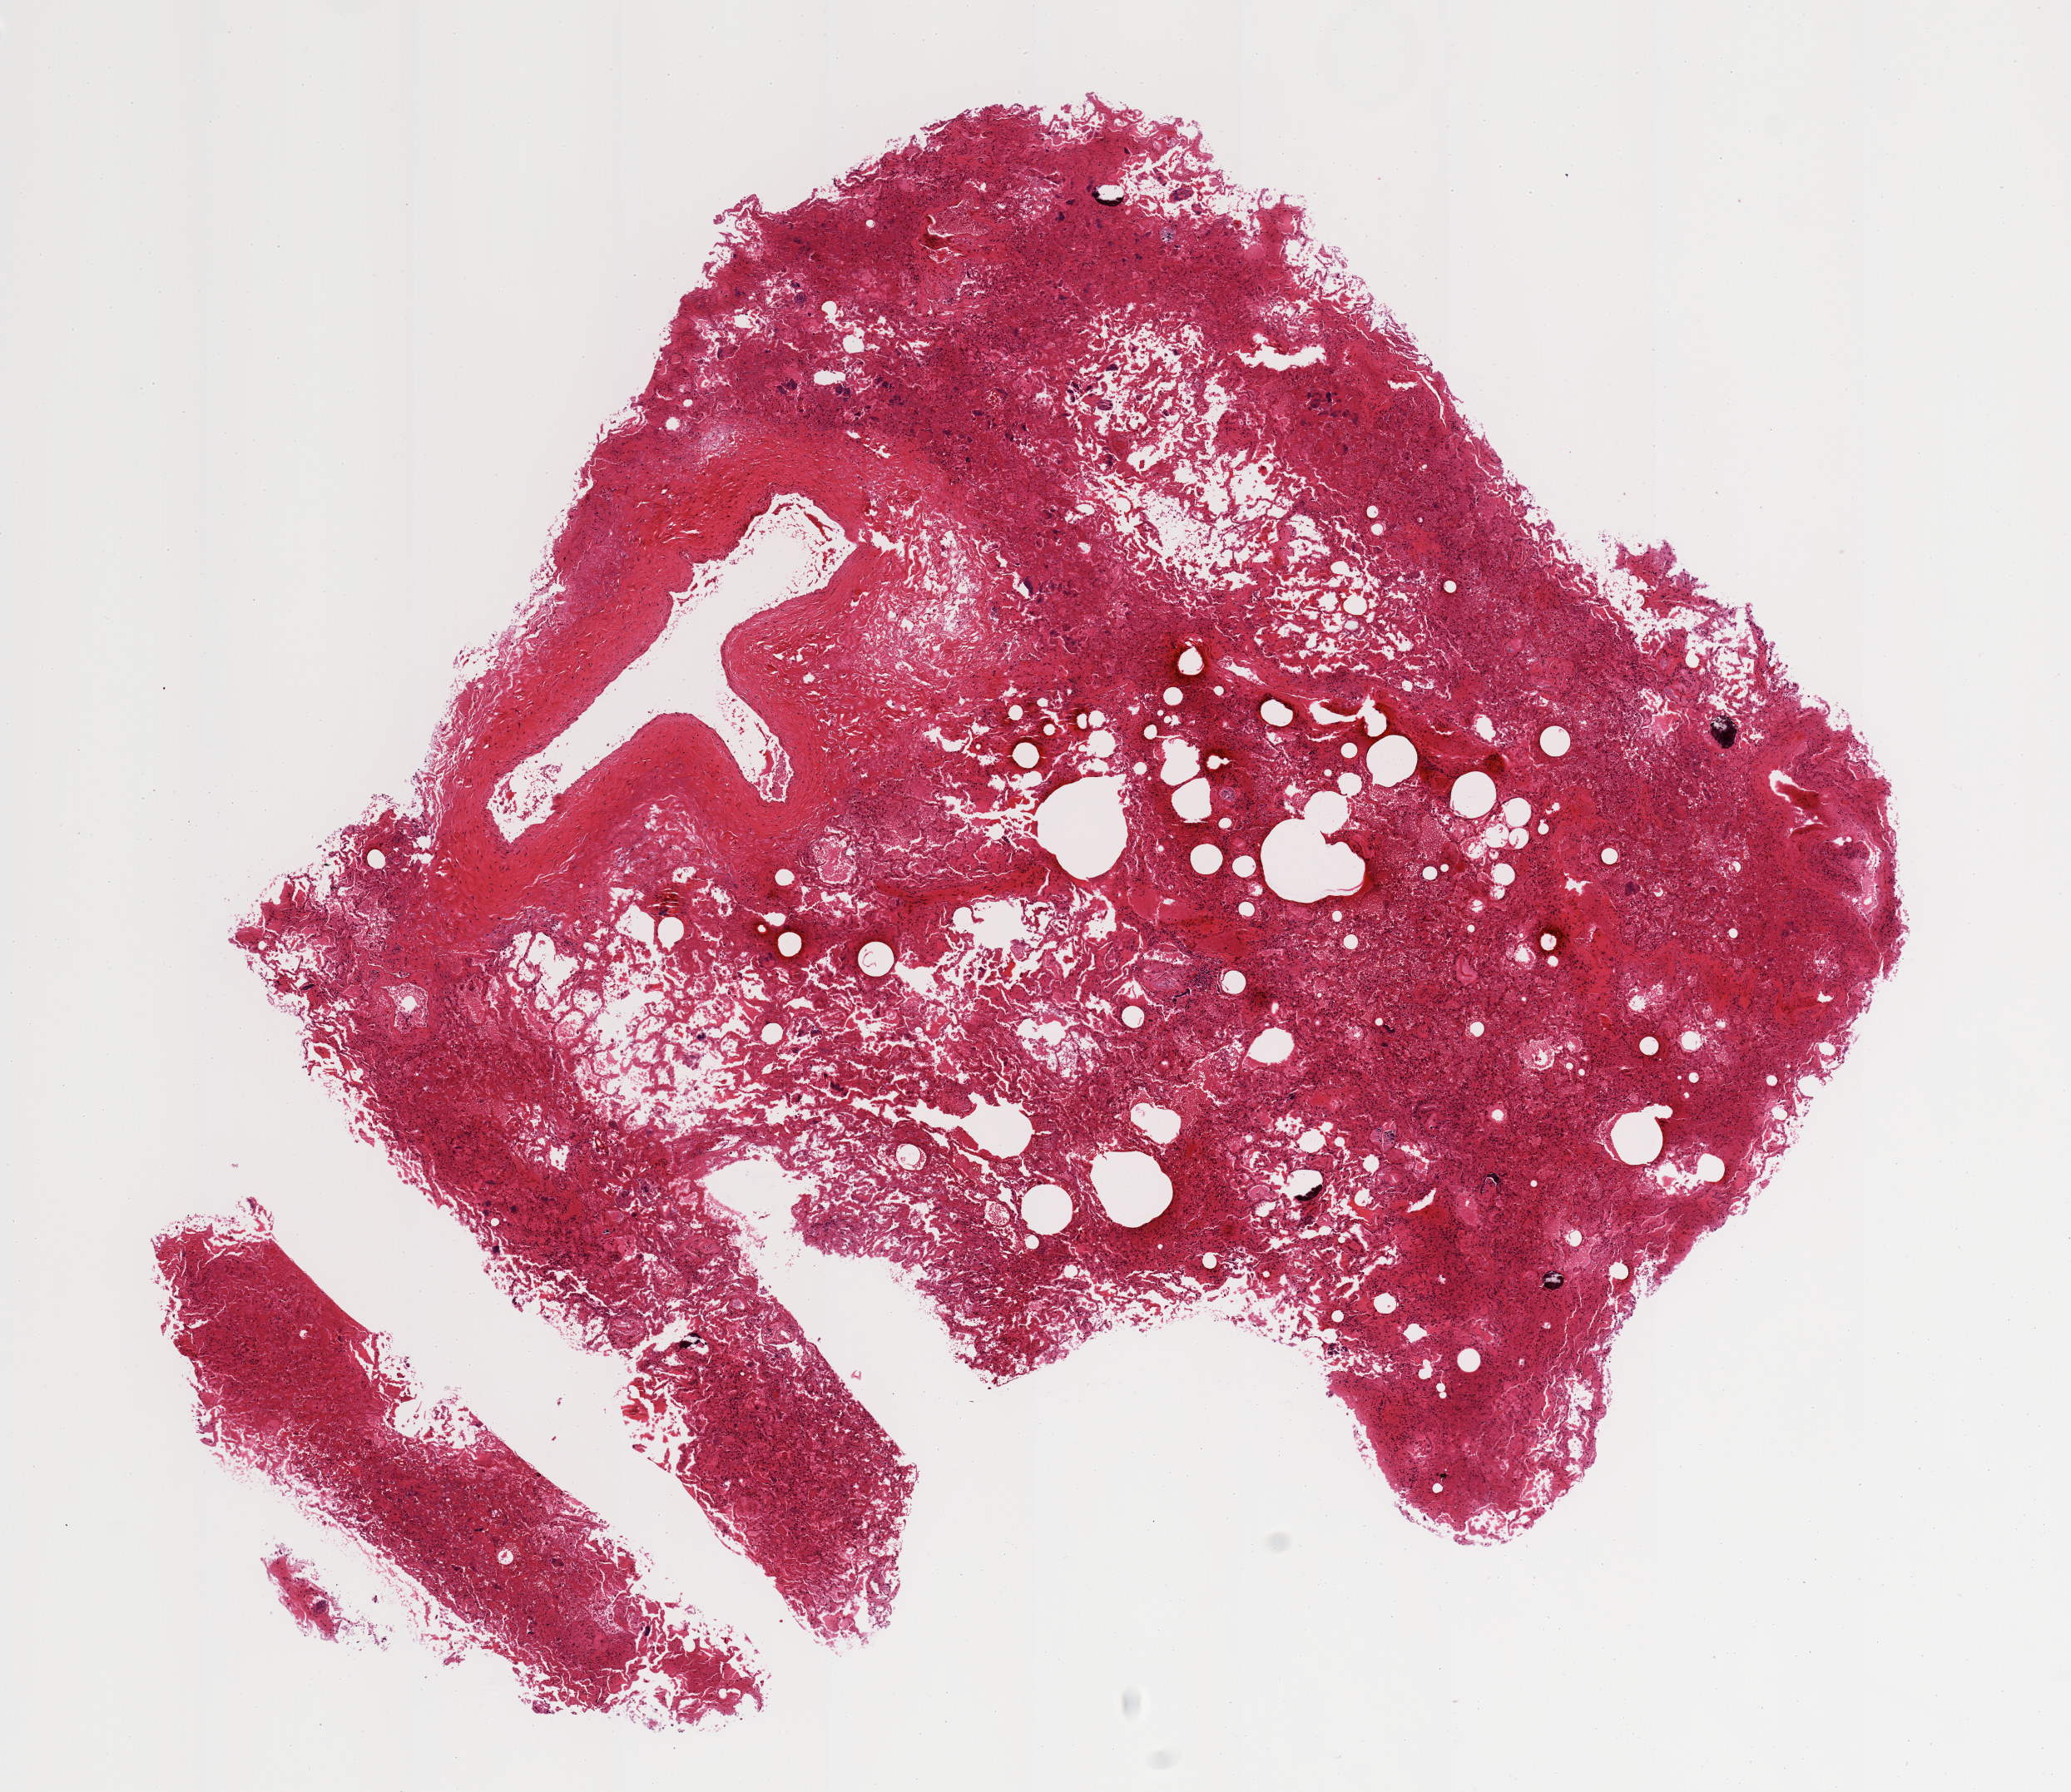
Whole-slide image, haematoxylin and eosin stain, low-resolution overview of the scanned area, about 9.8 x 8.5 mm, PAXgene-fixed, paraffin-embedded tissue, target tissue: lung, tissue donor sample.
Review note (as recorded): 7.6x6mm. Extremely hemorrhagic/edema? Pending glass review. Poorly fixed throughout.